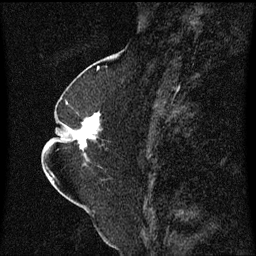
Breast MRI (dynamic contrast-enhanced), one sagittal slice; position 28 of 60 along the scan axis; dynamic contrast-enhanced series, image 2 of 3 at this slice position (ordered by acquisition); 1.5 T; TE 4.2 ms, TR 8.4 ms; 2 mm slice thickness; 256 × 256 image matrix. Patient: female, 52 years. Case-level facts recorded for this patient, not image findings: setting: breast cancer imaged before/during neoadjuvant chemotherapy; receptor status: HR-positive, HER2-negative.
Outlined on this slice (semi-automatically segmented with operator editing):
- analysis volume of interest (the breast-tissue region the enhancement analysis was run in; not a lesion): bounding box (x1, y1, x2, y2) in pixels: (64, 112, 108, 167)
- tumour enhancement mask (voxels above the 70 % enhancement threshold inside the analysis volume of interest): (77, 114, 101, 149)